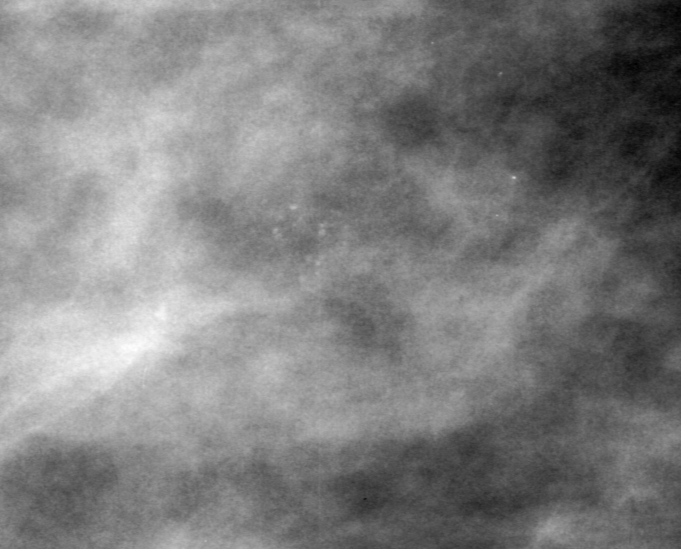
Region of interest cut from a scanned film mammogram (one marked finding), right breast, MLO view.
Finding: calcifications, morphology amorphous, distribution clustered; BI-RADS assessment category 3; pathology (as recorded): malignant.